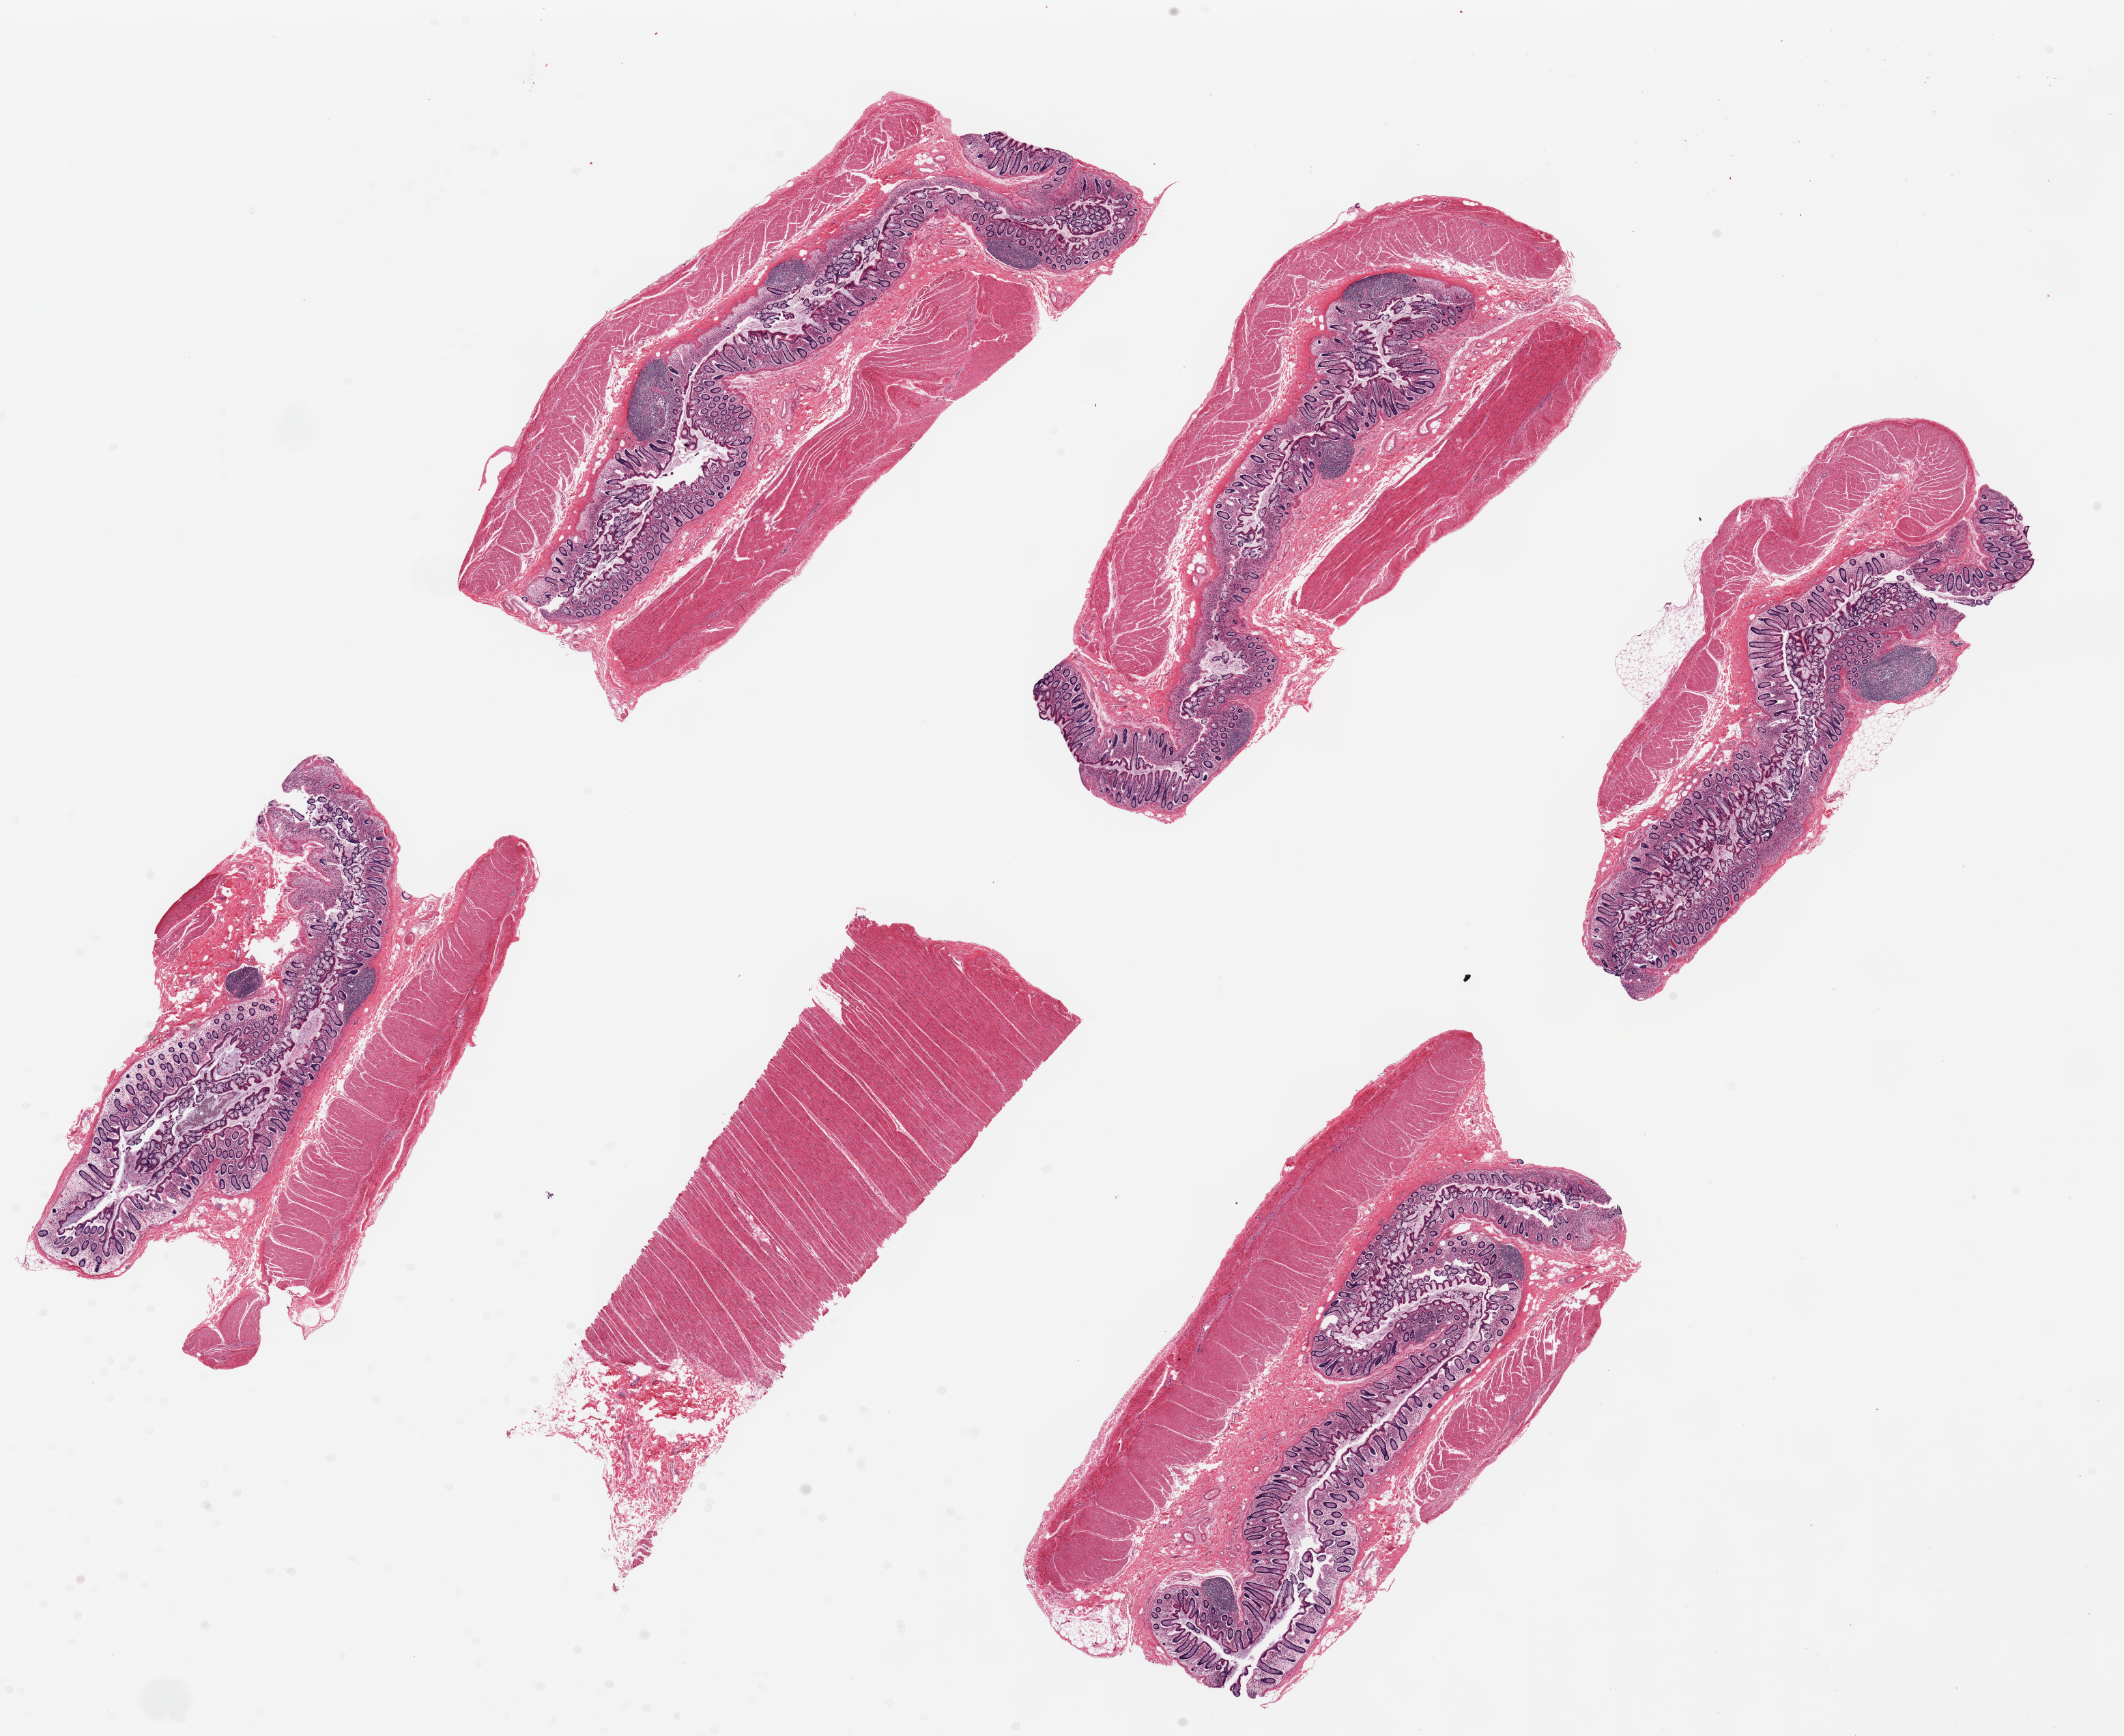
Haematoxylin and eosin whole-slide image, whole scanned area (about 24.6 x 20.1 mm) shown as a low-resolution overview; PAXgene-fixed paraffin-embedded (PFPE) section; section of transverse colon (target tissue); donor tissue sample. Donor sex: male.
* review note (as recorded): 6 ~8x2mm pieces; mucosa is 10-20% of thickness